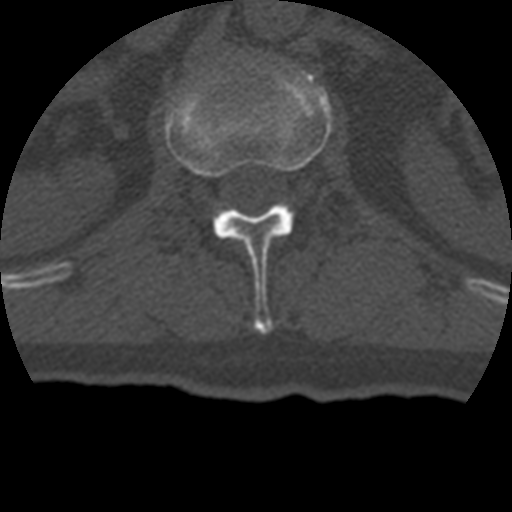
CT including the spine, one axial slice. Position 140 of 399 along the scan axis. Reconstruction kernel STANDARD. 120 kVp. Bone window (W 1800 / L 400 HU). 1.25 mm slice thickness. 512 × 512 image matrix. Patient age 69 years. Case-level facts recorded for this patient, not image findings: primary cancer: prostate.
Outlined on this slice (semi-automatic segmentation, software-assisted and operator-edited):
- L1 vertebra: box from (x=165, y=61) to (x=333, y=333) px